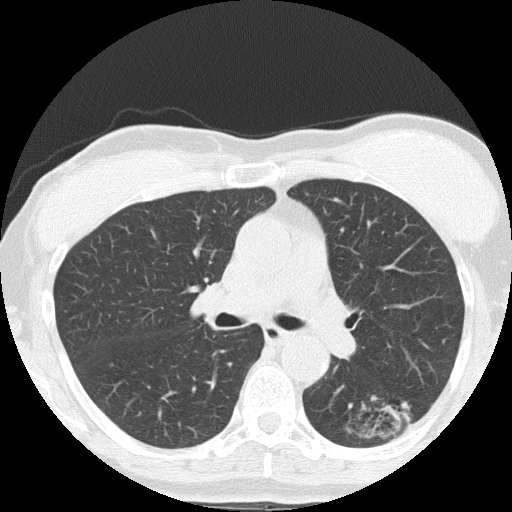
Low-dose screening chest CT, axial slice; third annual screen; lung window (W 1500 / L -600 HU); 2 mm slice thickness; lung (sharp) reconstruction kernel (FC51); slice 61 of 152 in the series; 512 × 512 image matrix. Female, age 64 years at enrolment.
Expert-annotated lung lesion, box from (x=352, y=380) to (x=439, y=451) px. The screening reader recorded 3 non-calcified nodules or masses ≥4 mm on this exam; which of them this box marks is not recorded. Official screen result: positive, other. Lung cancer was diagnosed 212 days after this screen: adenocarcinoma, NOS, left lower lobe, moderately differentiated (G2), stage IA (AJCC 6th edition), 17 mm at pathology.